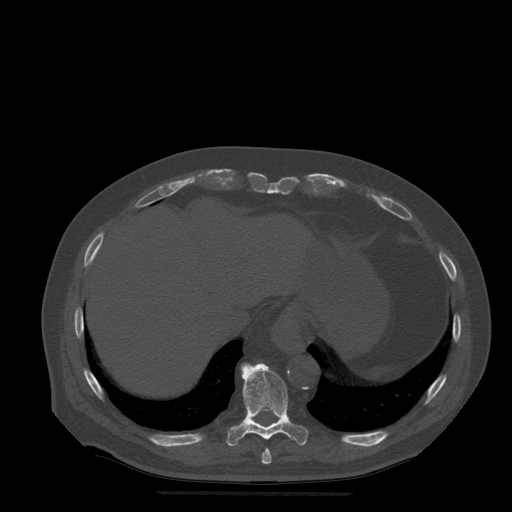
CT including the spine, one axial slice; bone window (W 1800 / L 400 HU); 512 × 512 image matrix. Patient age 72 years. From the clinical record (not read from this slice): primary cancer: prostate.
Annotated regions visible in this slice (semi-automatic segmentation, software-assisted and operator-edited):
- T10 vertebra: box from (x=227, y=363) to (x=308, y=447) px
- T9 vertebra: (x=262, y=449)–(x=272, y=464)